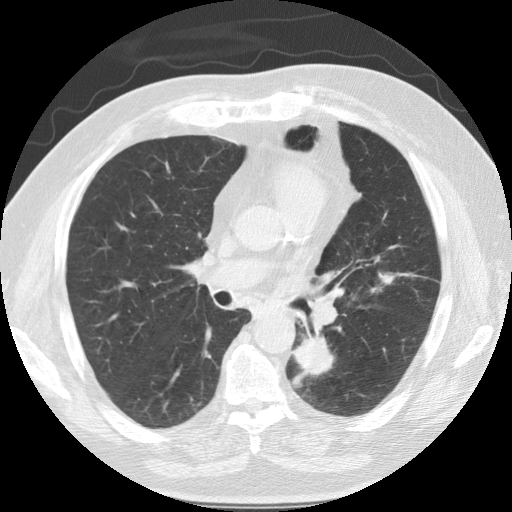
Low-dose screening chest CT, one axial slice; slice 67 of 124 in the series (ordered by position); reconstruction kernel STANDARD; 120 kVp; lung window (W 1500 / L -600 HU); 2.5 mm slice thickness; 512 × 512 image matrix.
Structures marked on this image (expert manual segmentation):
- lesion 1 (tumor, lower lobe of left lung): bounding box (x1, y1, x2, y2) in pixels: (291, 337, 335, 388)